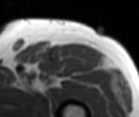
MRI of an extremity soft-tissue mass, one axial slice; slice 77 of 86 in the series (ordered by position); MR volume resampled by the dataset authors to the PET/CT grid (not the native acquisition matrix); 3.27 mm slice thickness; 139 × 117 image matrix. Male patient. From the clinical record (not read from this slice): histological type: extraskeletal osteosarcoma; grade: high; site of the primary tumour: thigh.
Annotated regions visible in this slice (expert contour drawn on MRI and transferred to this co-registered scan by the dataset authors):
- gross tumour volume (mass): bounding box [x1, y1, x2, y2] px = [58, 43, 103, 67]